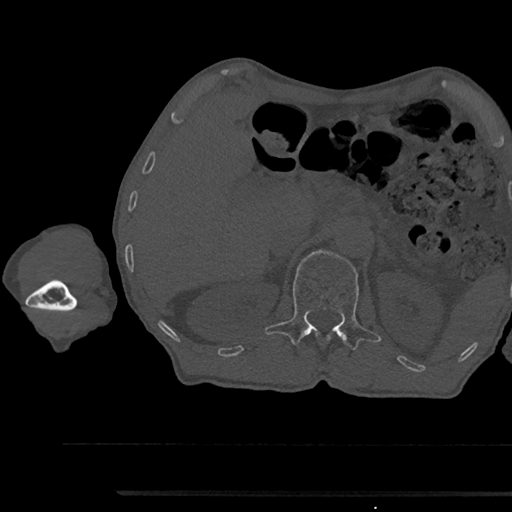
CT including the spine, one axial slice. 120 kVp. Bone window (W 1800 / L 400 HU). 0.5 mm slice thickness. 512 × 512 image matrix, field of view 367 × 367 mm. Male patient, age 79 years. From the clinical record (not read from this slice): primary cancer: prostate.
Structures marked on this image (semi-automatic segmentation, software-assisted and operator-edited):
- L1 vertebra: box from (x=264, y=250) to (x=381, y=350) px